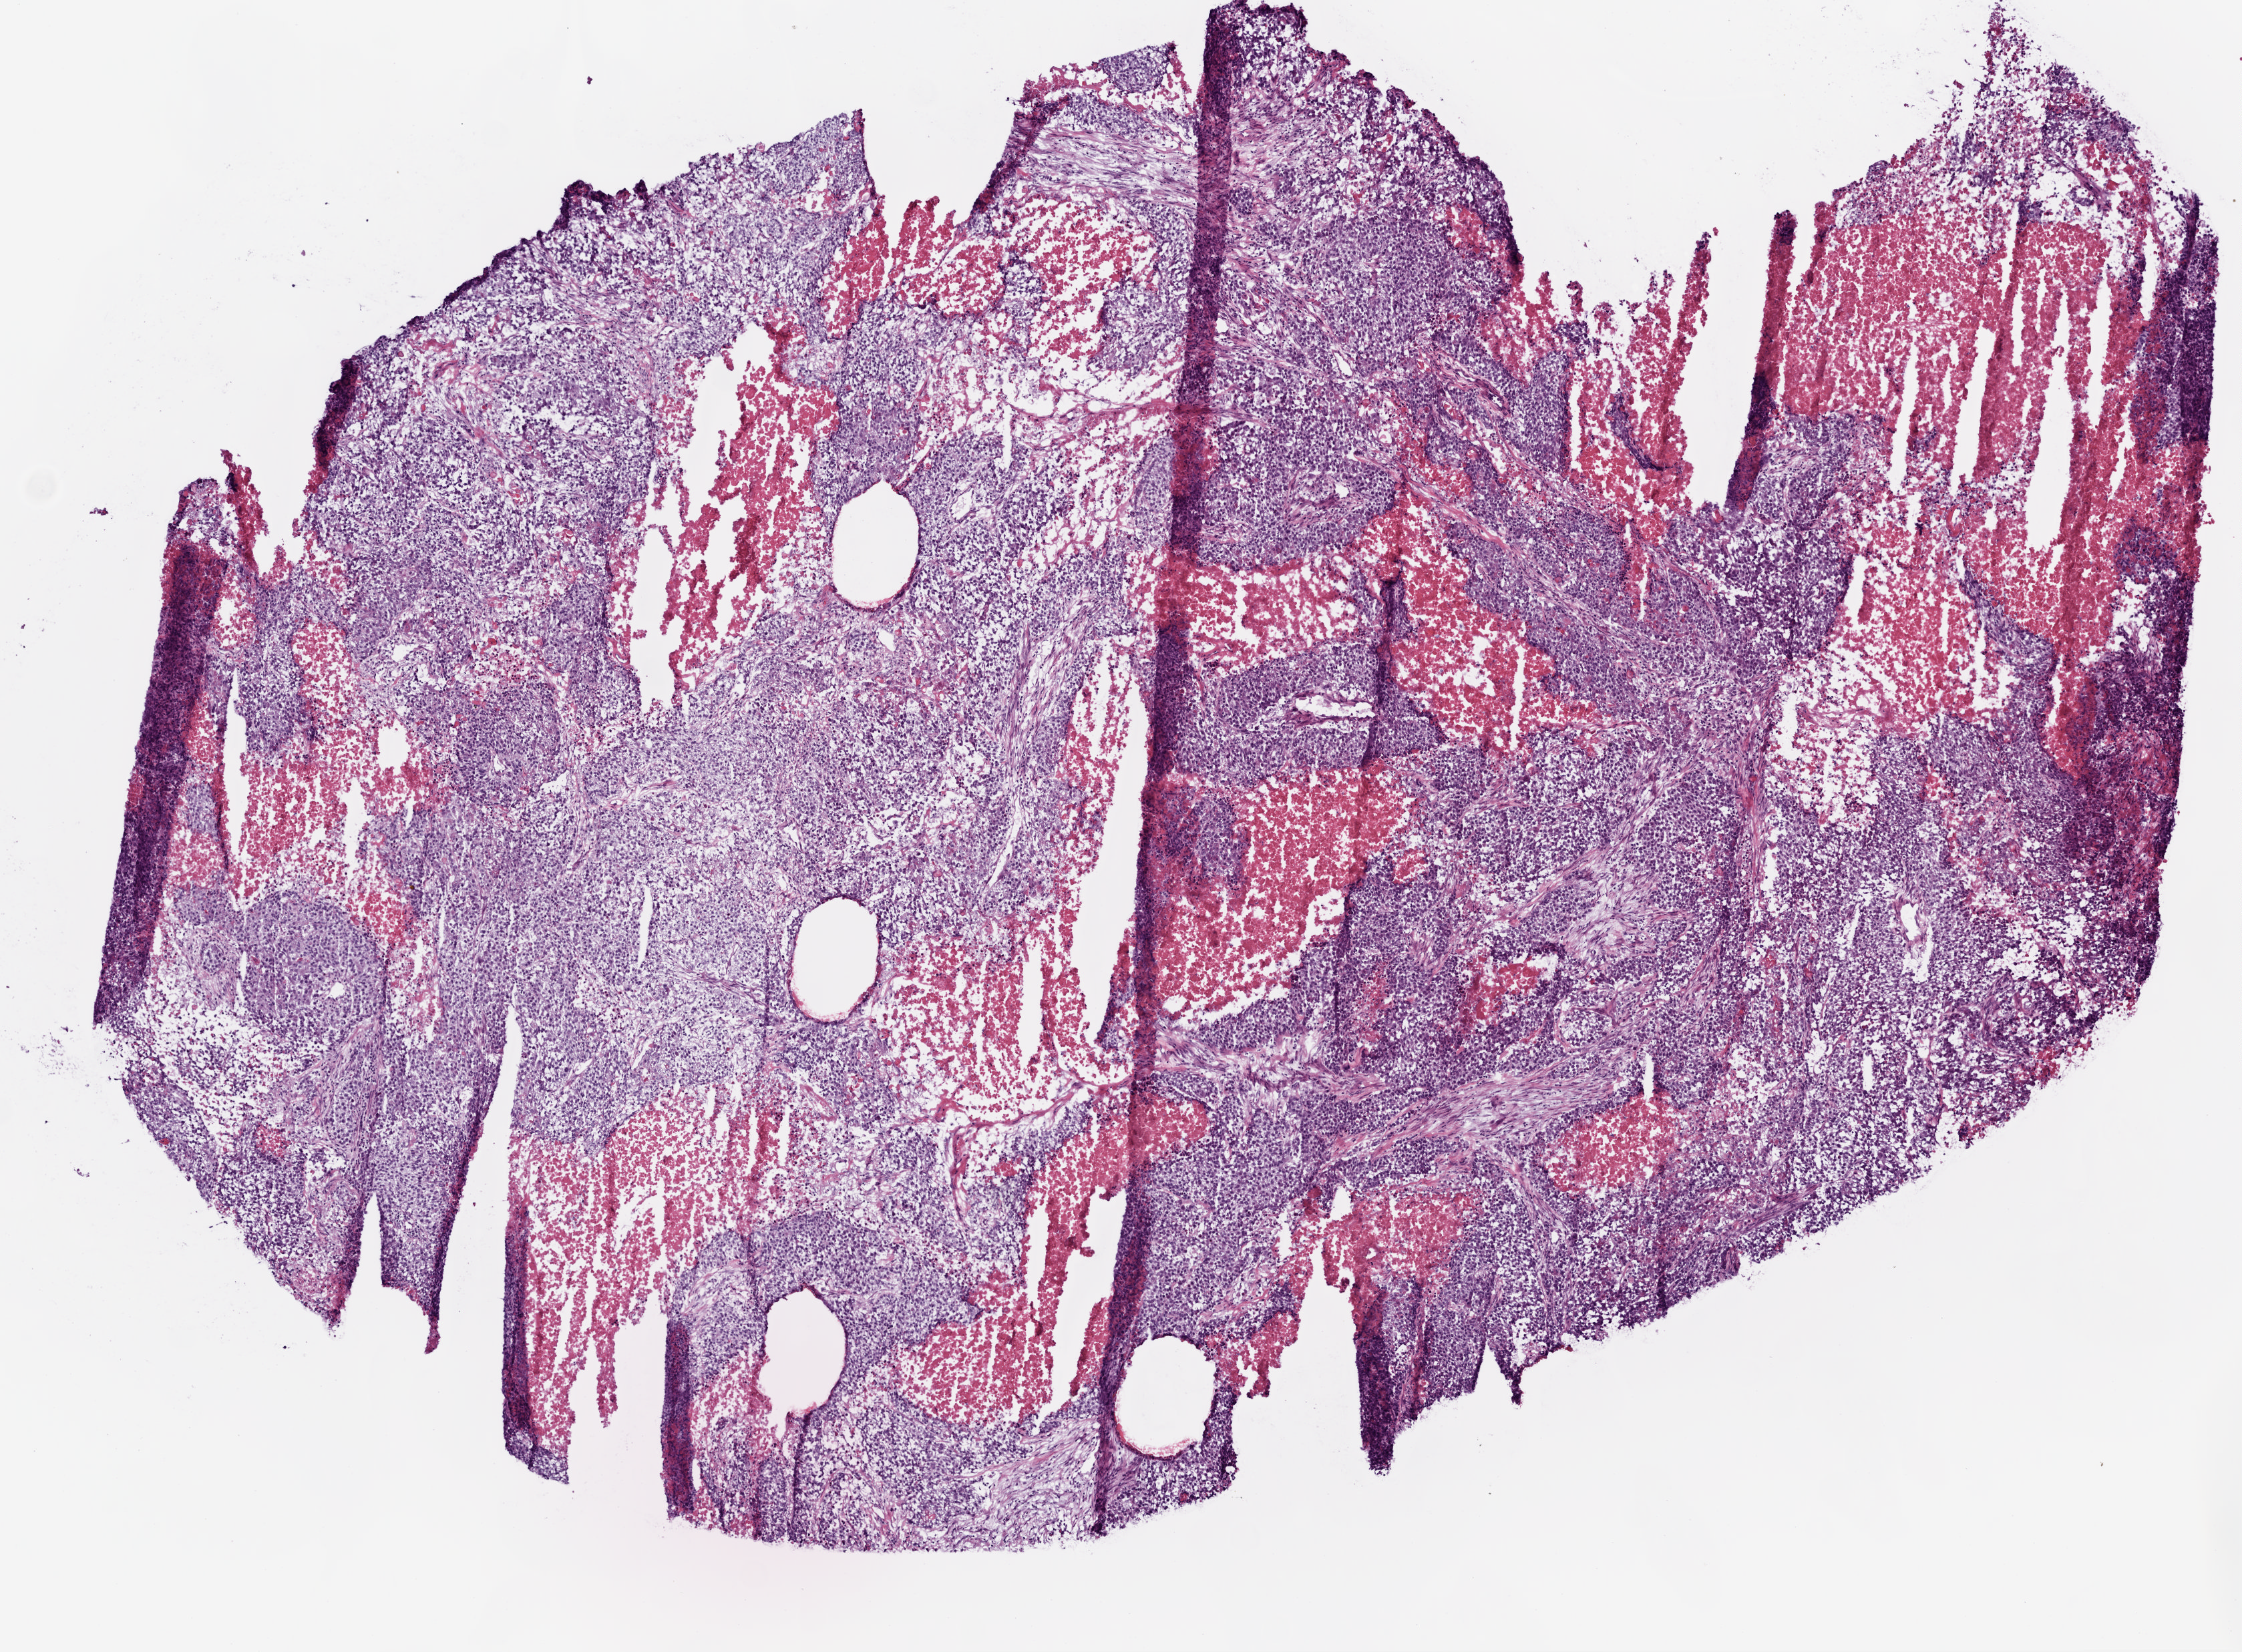
Digitized H&E tissue section (whole slide), shown as a low-resolution overview of the whole scanned area (about 6.8 x 5.0 mm), frozen section from the top of the tissue portion, sample: primary tumour, cervix. Patient: female, age at initial diagnosis 64 years. Histologic grade: G3 (poorly differentiated). Slide review estimates, as recorded: tumour cells 75%, tumour nuclei 80%, normal cells 0%, stromal cells 15%, necrosis 10%. Infiltration values recorded for this section: lymphocyte infiltration 0%, monocyte infiltration 0%, neutrophil infiltration 0%.
Histologic diagnosis: Squamous cell carcinoma, large cell, nonkeratinizing, NOS (cervix uteri). Lymph nodes positive (case pathology): 0 of 9 examined. FIGO stage: IIA2.